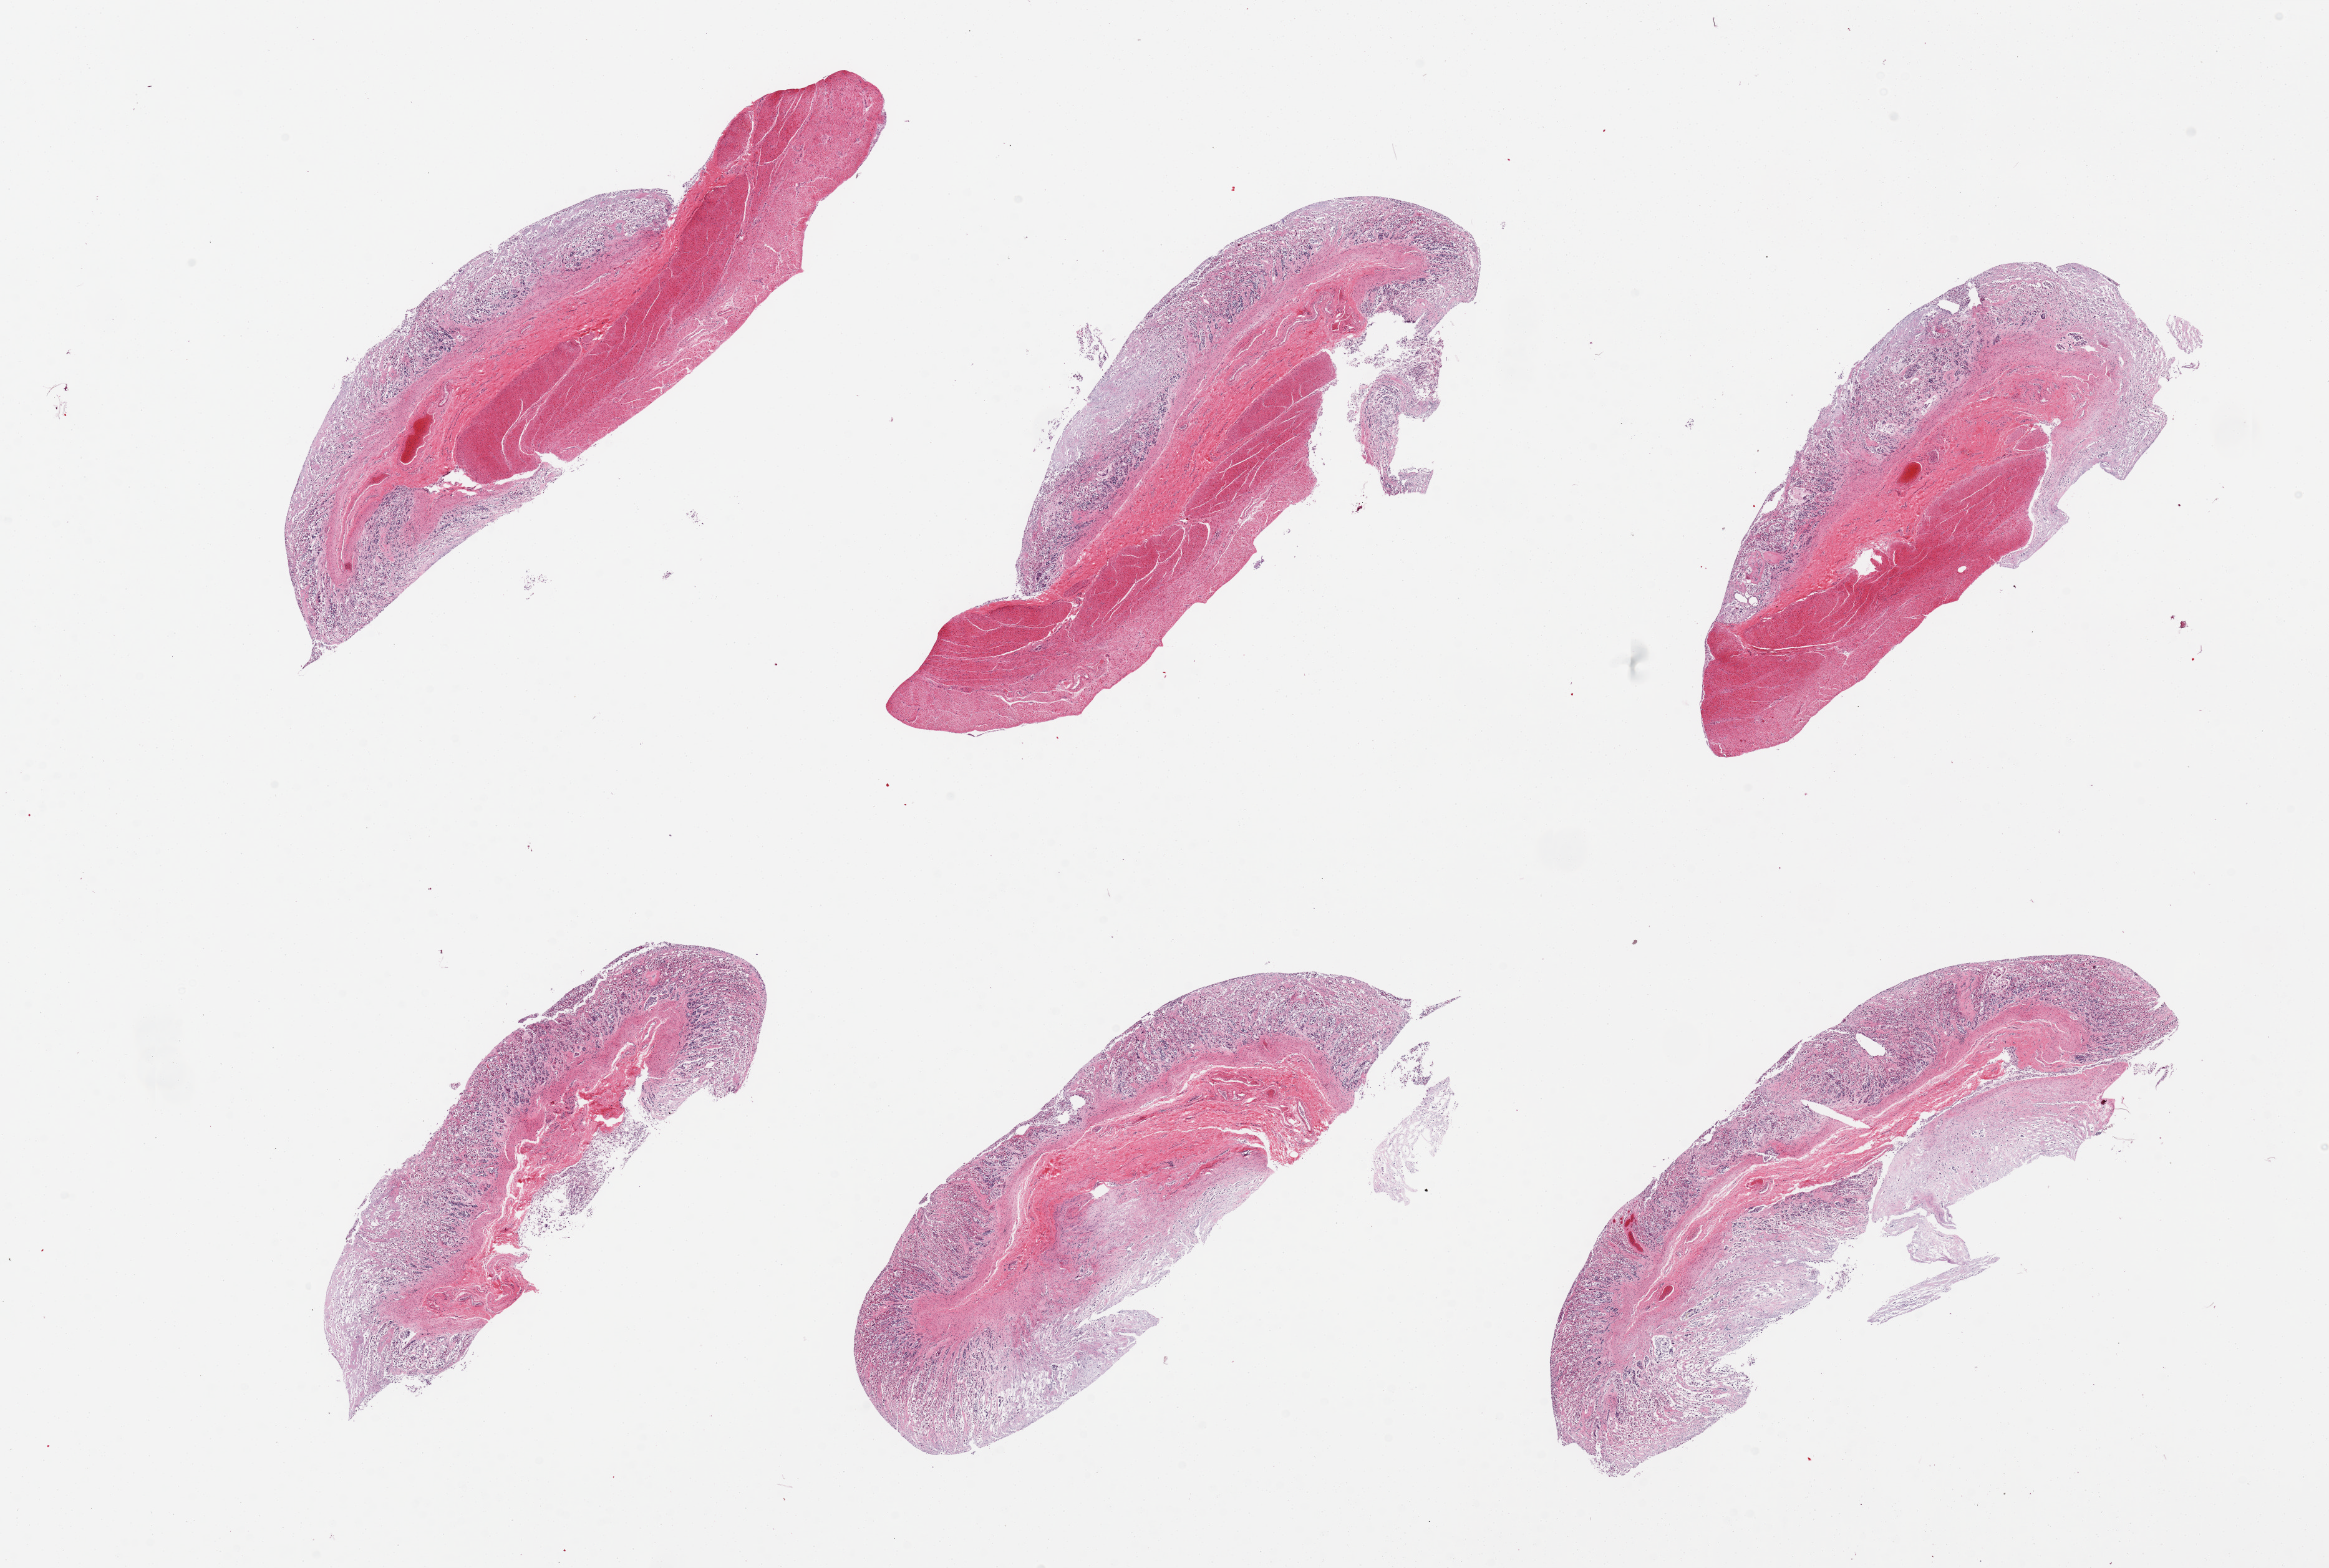
Haematoxylin and eosin whole-slide image — low-resolution overview of the scanned area, about 29.5 x 19.9 mm; PAXgene-fixed, paraffin-embedded tissue; target tissue: stomach; donor tissue sample. Donor: male.
* reviewer comment on this tissue sample: 6 pieces. Mucosa up to ~70% thickness but completely autolyzed